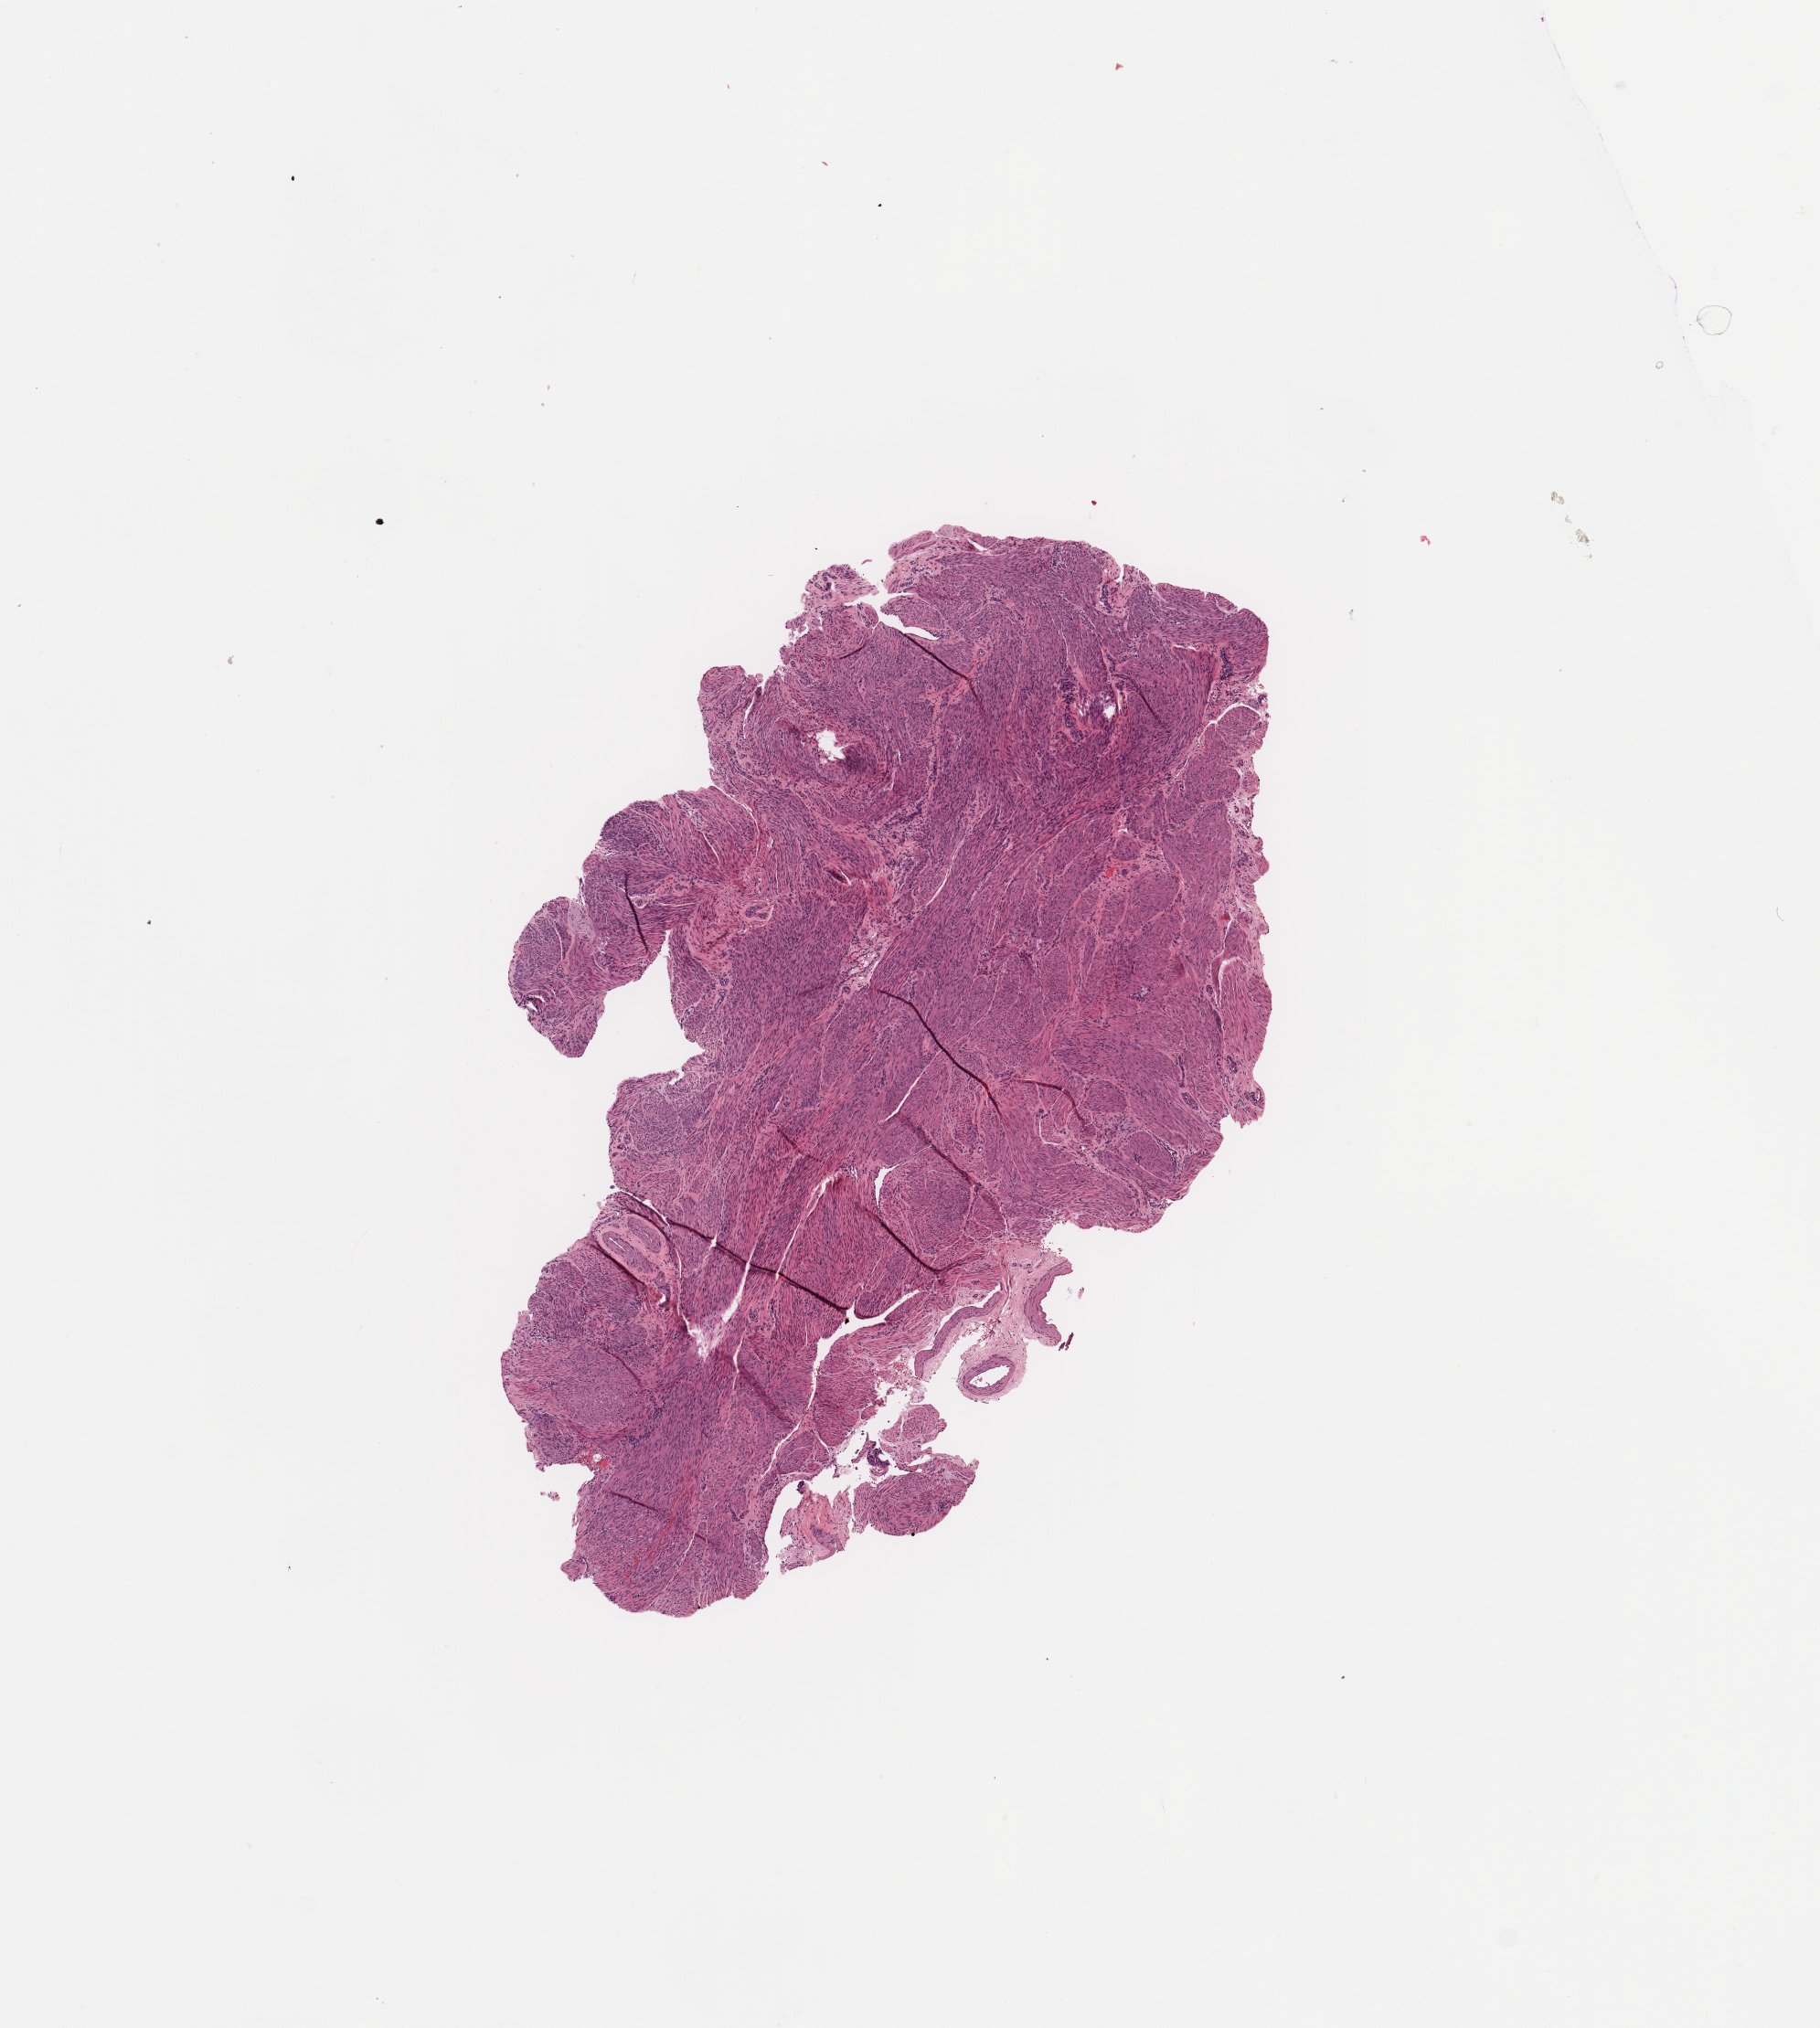
Whole-slide histology image, Hematoxylin and eosin (H&E) stained, low-resolution overview of the scanned area, about 7.9 x 8.8 mm. Normal (non-tumour) tissue sample, uterus. Female, 54 y/o.
- this section: normal (non-tumour) tissue from the same patient
- patient diagnosis: Endometrioid adenocarcinoma, NOS